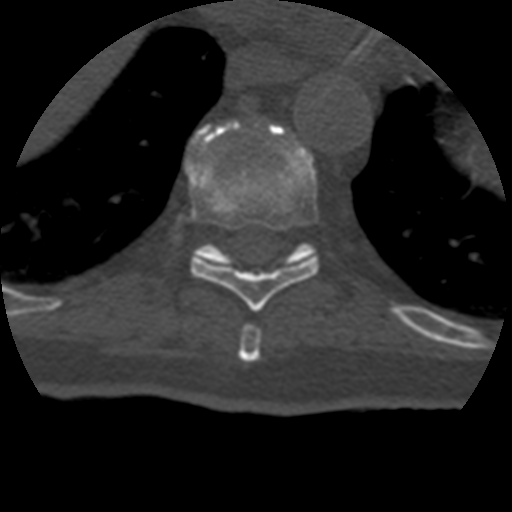
CT including the spine, one axial slice; position 234 of 399 along the scan axis; reconstruction kernel STANDARD; bone window (W 1800 / L 400 HU); 1.25 mm slice thickness; 512 × 512 image matrix, field of view 160 × 160 mm. Patient age 69 years. Case-level facts recorded for this patient, not image findings: primary cancer: prostate.
Annotated regions visible in this slice (semi-automatically segmented with operator editing):
- T10 vertebra: bounding box [x1, y1, x2, y2] px = [193, 124, 316, 266]
- T8 vertebra: [238, 325, 262, 362]
- T9 vertebra: [190, 143, 319, 312]